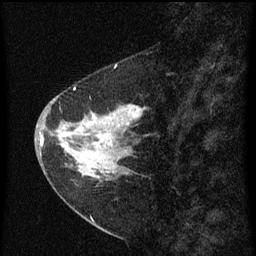
Breast MRI (dynamic contrast-enhanced), one sagittal slice. Position 23 of 60 along the scan axis. Dynamic contrast-enhanced series, image 2 of 3 at this slice position (ordered by acquisition). 1.5 T. TE 4.2 ms, TR 8 ms. 2 mm slice thickness. 256 × 256 image matrix. Female patient, age 47 years.
Structures marked on this image (semi-automatically segmented with operator editing):
- analysis volume of interest (the breast-tissue region the enhancement analysis was run in; not a lesion): bounding box [x1, y1, x2, y2] px = [44, 84, 149, 199]
- tumour enhancement mask (voxels above the 70 % enhancement threshold inside the analysis volume of interest): [44, 88, 147, 175]